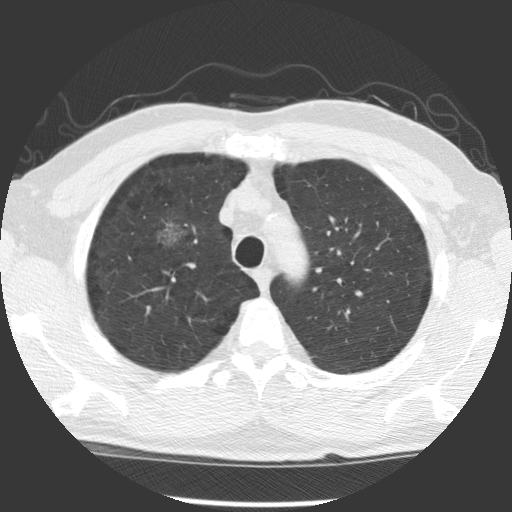
Axial slice from a low-dose chest CT screening exam; baseline annual screen; lung window (W 1500 / L -600 HU); 2.5 mm slice thickness; slice 90 of 122 in the series. Male, age 60 years at enrolment. Former smoker at enrolment.
Expert-annotated lung lesion, bounding box <141,210,205,262> (left, top, right, bottom; pixels). Reader record for this screening exam (exam-level; its link to the box is not recorded): non-calcified nodule or mass ≥4 mm, right middle lobe, 20 × 20 mm, poorly defined margins, ground glass attenuation. Official screen result: positive, change unspecified: nodule(s) >= 4 mm or enlarging nodule(s), mass(es), or other non-specific abnormalities suspicious for lung cancer. Later outcome: lung cancer diagnosed 863 days after this screen — papillary adenocarcinoma, NOS, right upper lobe, moderately differentiated (G2), stage IB (AJCC 6th edition), 32 mm at pathology.